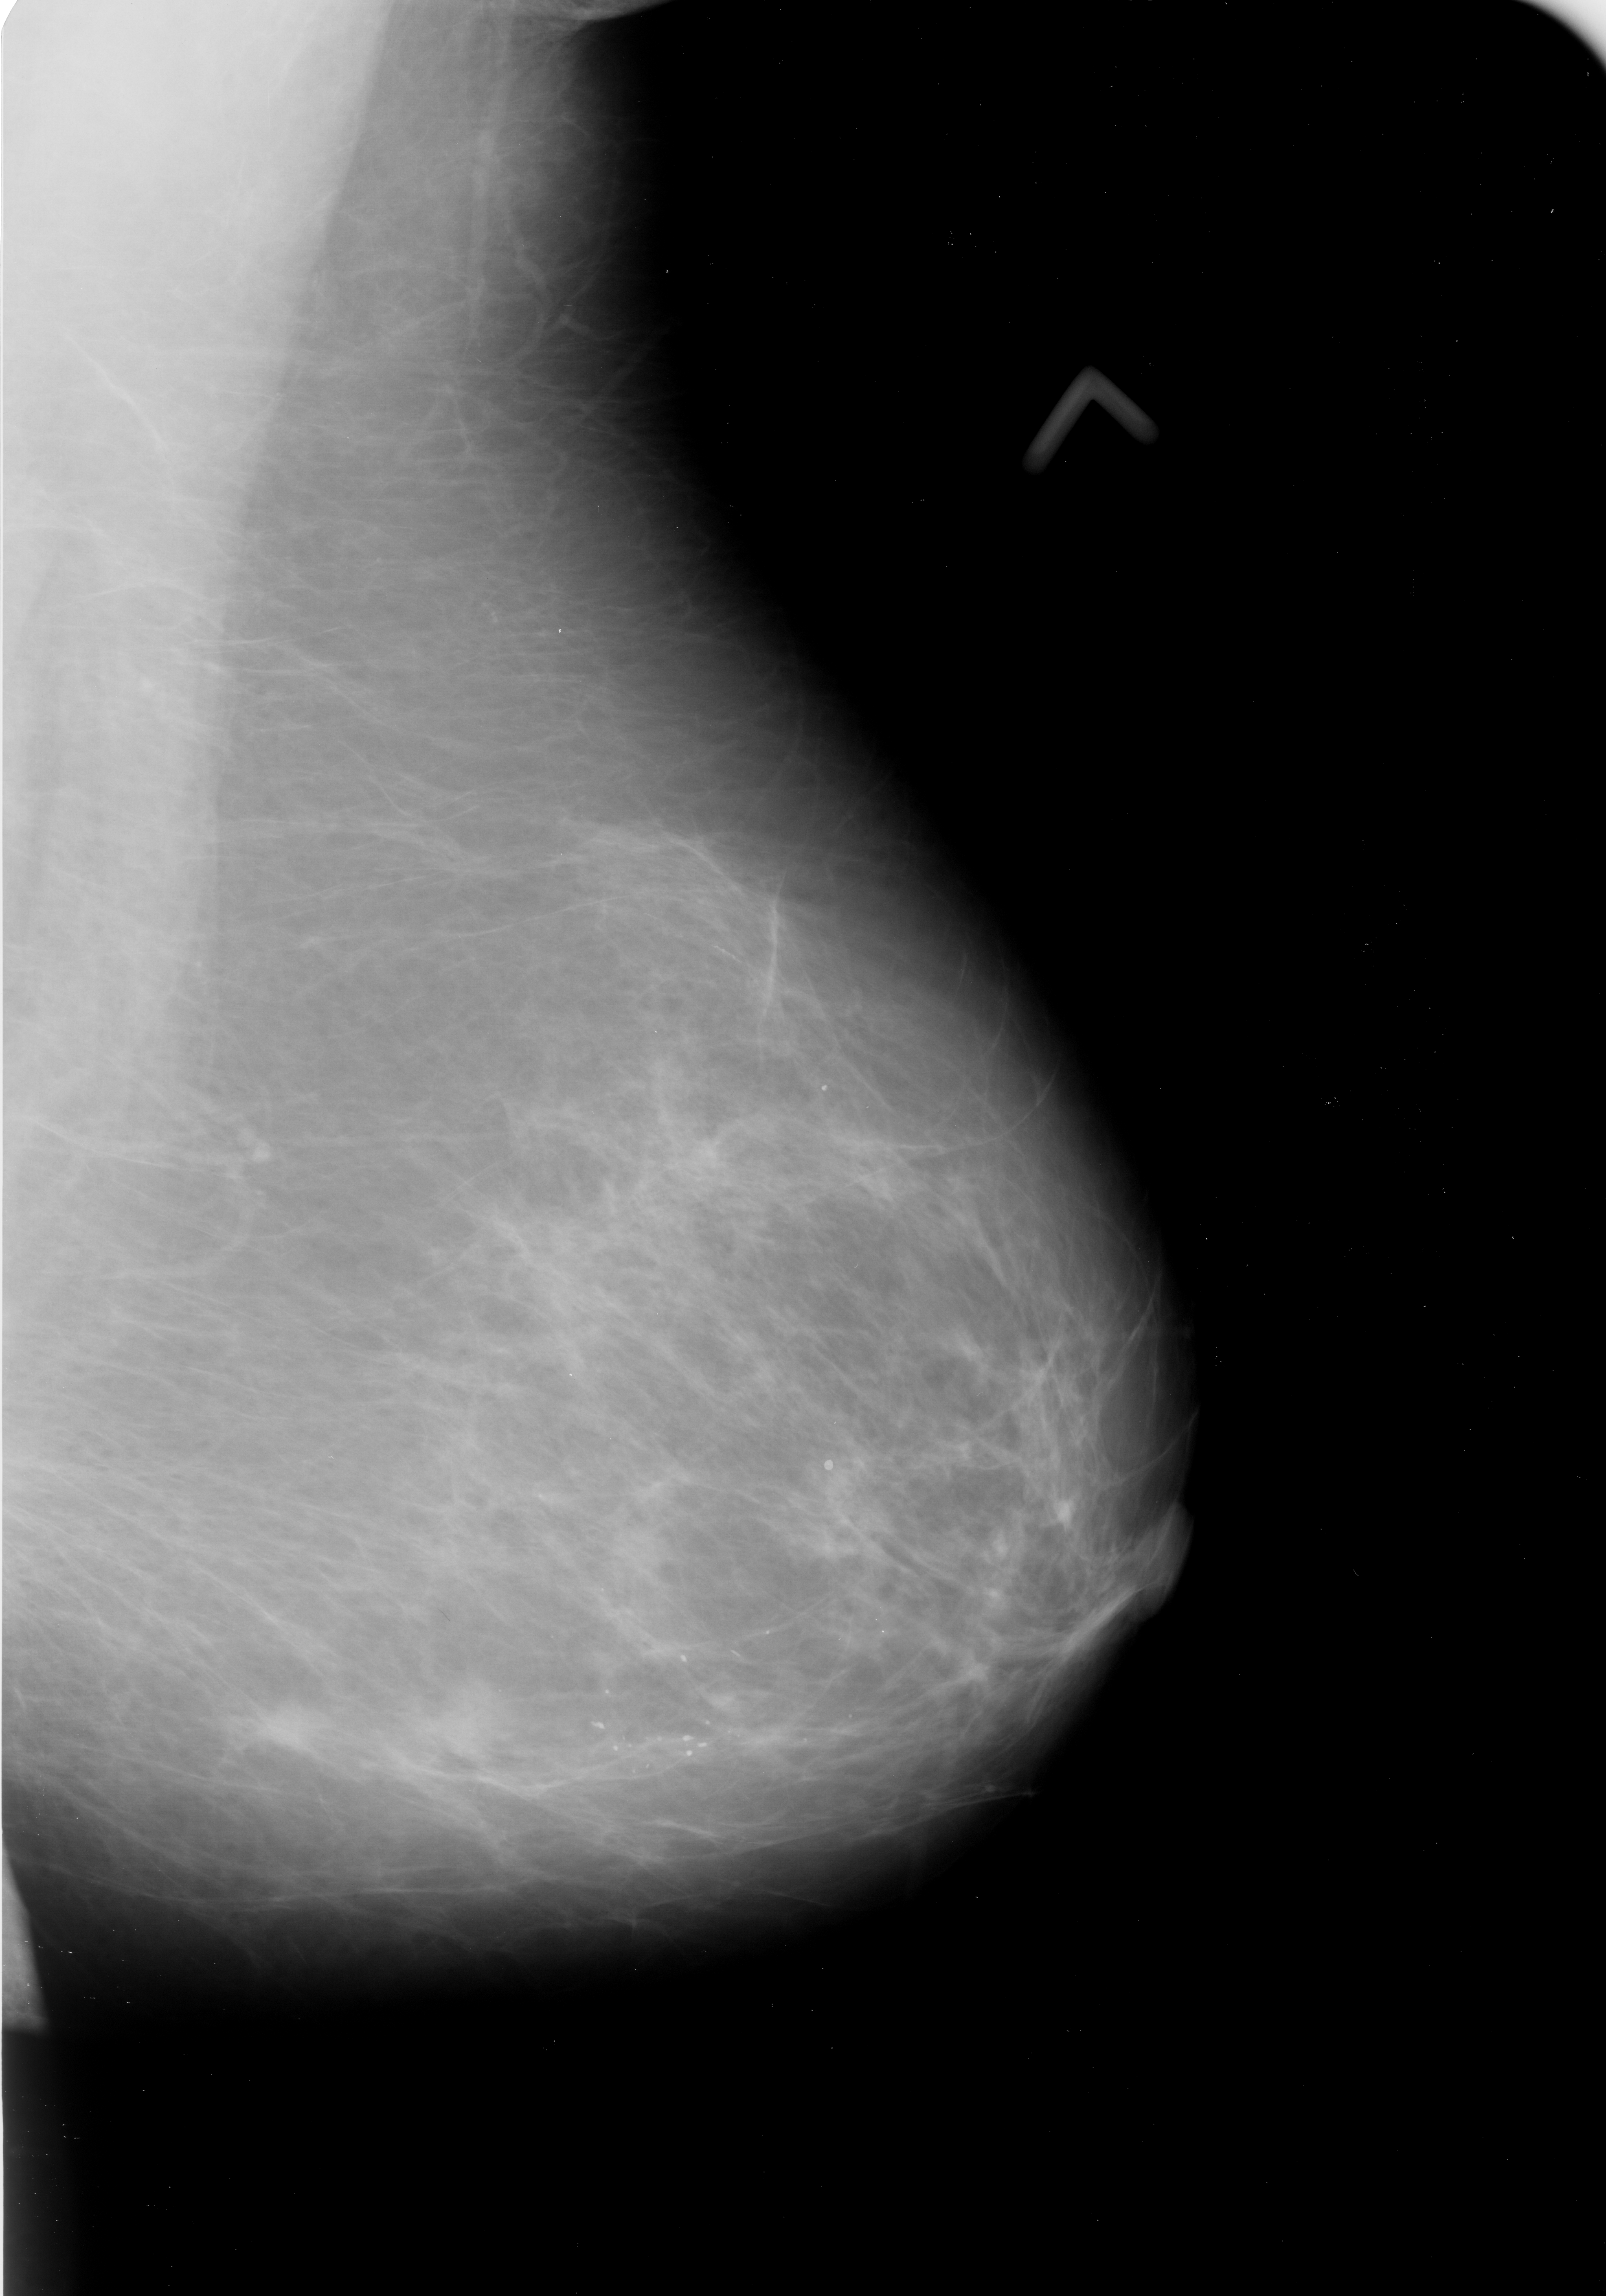
Mammogram (digitized film); left breast; mediolateral oblique (MLO) view.
- Abnormality record for this image: Finding 1 of 2: mass, shape irregular, margins spiculated; BI-RADS assessment category 4; pathology (as recorded): malignant.
- Finding 2 of 2: mass, shape irregular, margins spiculated; BI-RADS assessment category 4; subtlety rating 3 on a 1 (subtle) to 5 (obvious) scale; pathology (as recorded): malignant.